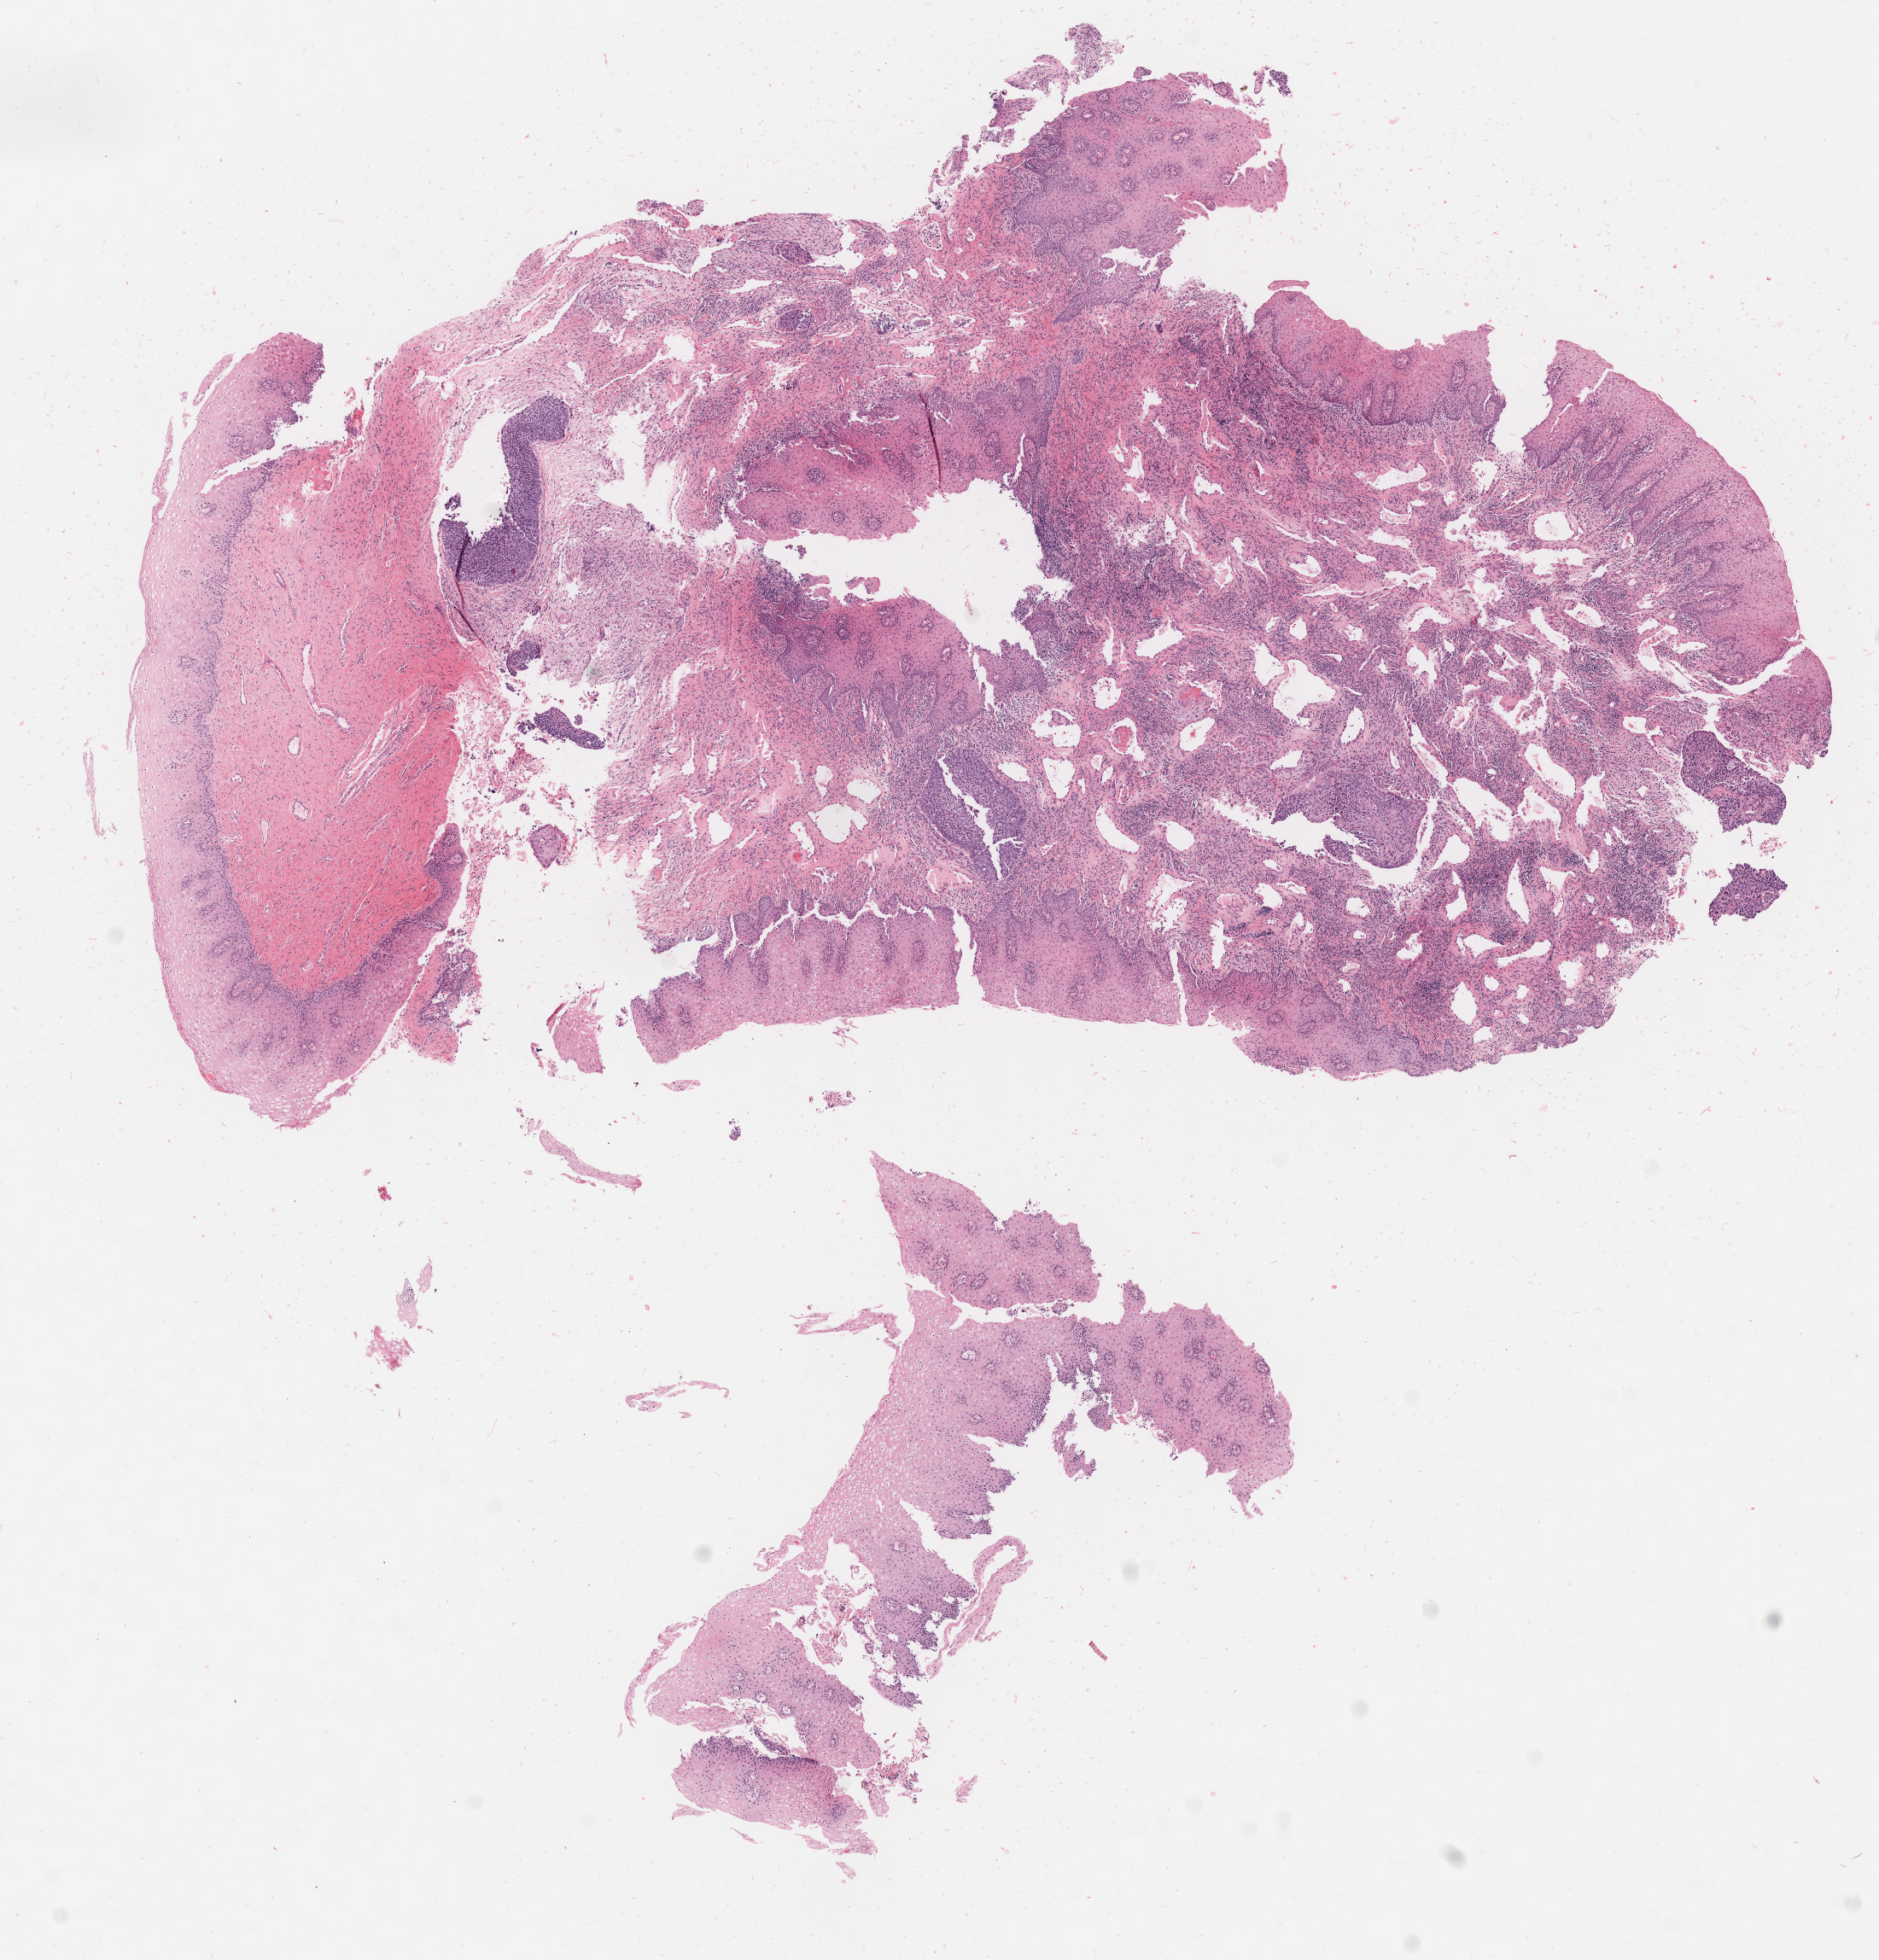
Hematoxylin and eosin (H&E) whole-slide image, whole scanned area (about 8.8 x 9.1 mm) shown as a low-resolution overview, specimen: tumor tissue, anatomic site: cervix. Patient: female, age 47 years.
Diagnosis: Squamous cell carcinoma, large cell, nonkeratinizing, NOS.